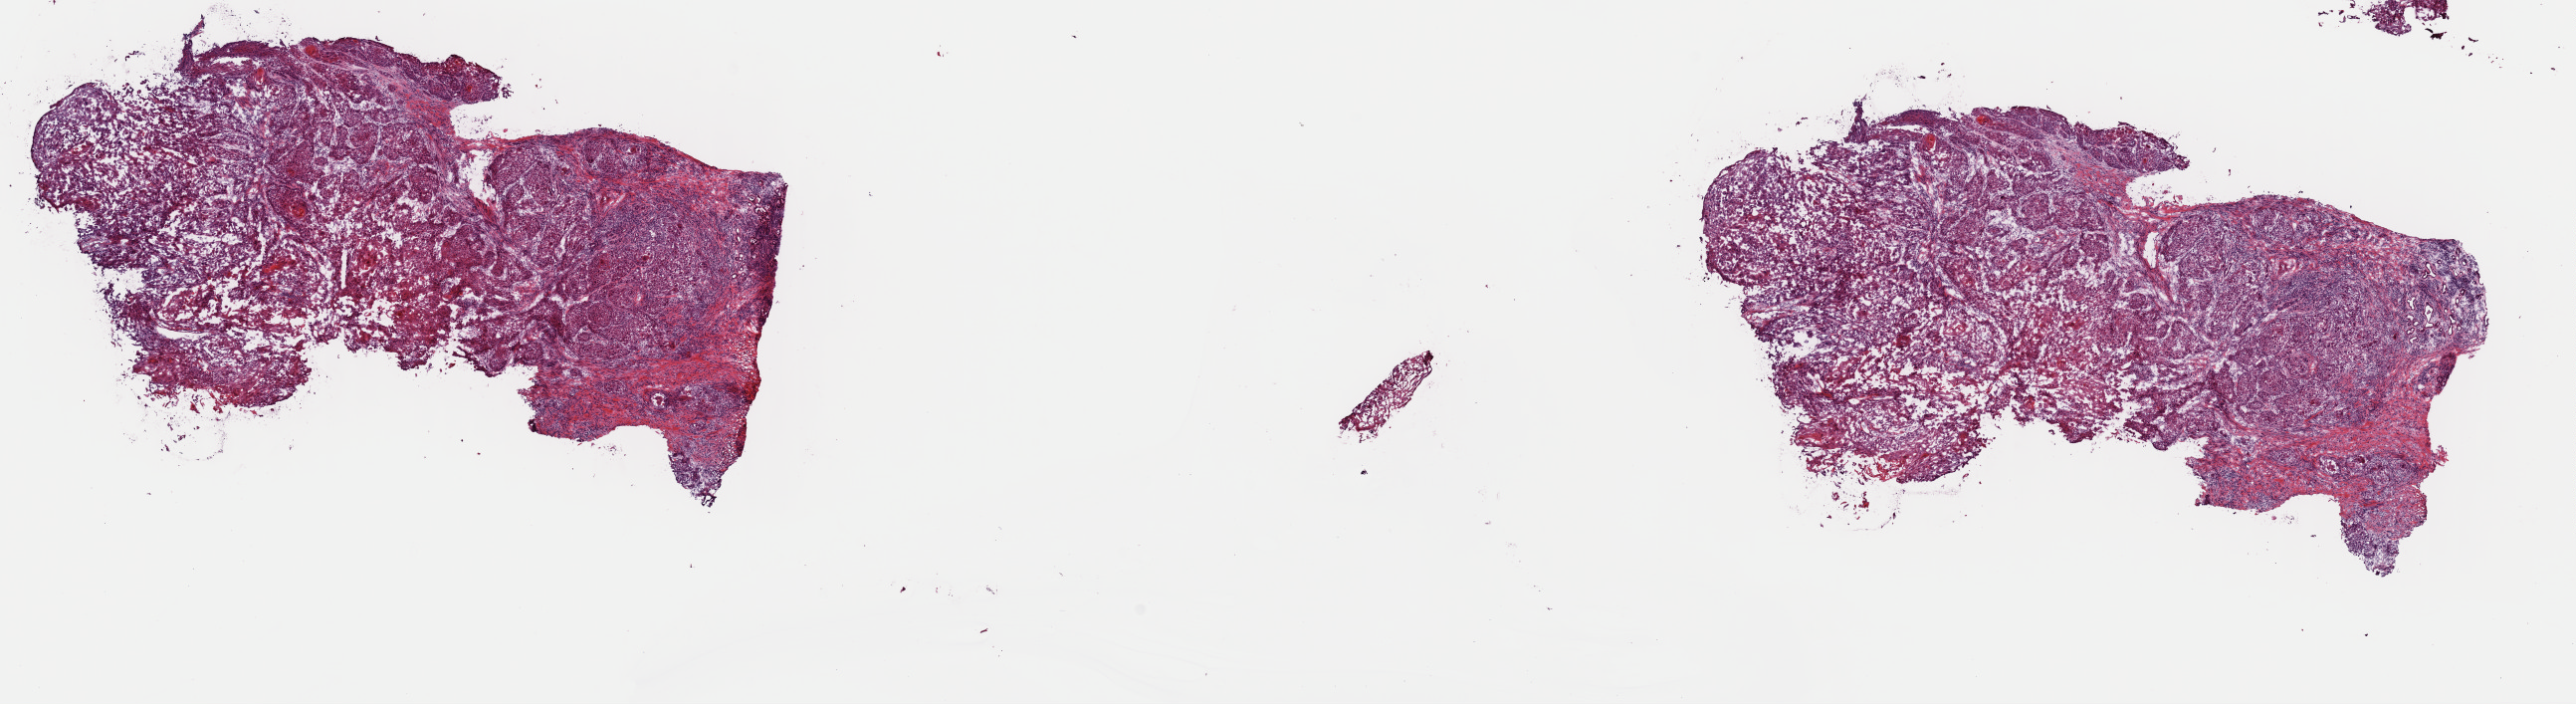
Digitized H&E tissue section (whole slide), whole scanned area (about 20.4 x 5.6 mm, acquisition: 40x scan) shown as a low-resolution overview. Frozen section from the top of the tissue portion. Primary tumour sample from the head and neck. Patient: male, age at initial diagnosis 57 years. Histologic grade: G3 (poorly differentiated). Pathologist review of this section (percent, as recorded): tumour cells 100%, tumour nuclei 80%, normal cells 0%, stromal cells 0%, necrosis 0%. Inflammatory infiltration, as recorded: lymphocyte infiltration 4%, monocyte infiltration 0%, neutrophil infiltration 0%.
Diagnosis: Squamous cell carcinoma, keratinizing, NOS (larynx, NOS). AJCC pathologic stage: IVA (7th edition).